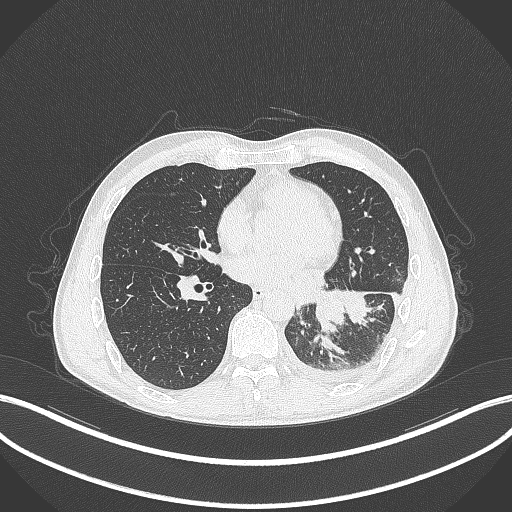
Chest CT, one axial slice. Slice 133 of 295 in the series (ordered by position). 120 kVp. Lung window (W 1500 / L -600 HU). 512 × 512 image matrix, field of view 400 × 400 mm. Patient: male, 47 years. From the clinical record (not read from this slice): clinical TNM (as recorded): T3 N1 M1c.
Annotated regions visible in this slice (bounding box drawn by a radiologist):
- lung tumour (recorded histology: small cell carcinoma): box from (x=312, y=289) to (x=347, y=333) px